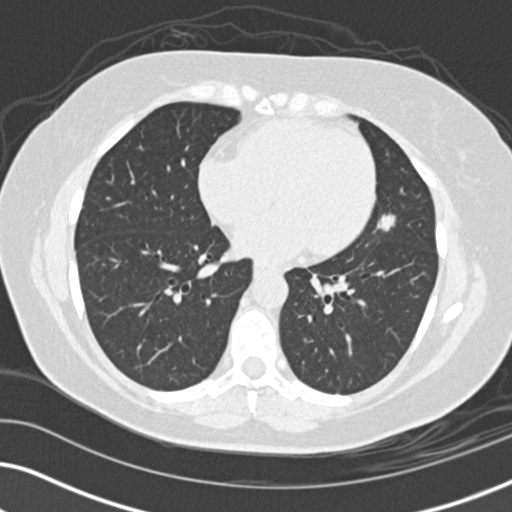
Low-dose screening chest CT, one axial slice; slice 69 of 152 in the series (ordered by position); reconstruction kernel B30f; 120 kVp; lung window (W 1500 / L -600 HU); 2 mm slice thickness; 512 × 512 image matrix.
Structures marked on this image (outlined manually by an expert reader):
- lesion 1 (tumor, upper lobe of left lung): bounding box <377,213,396,231> (left, top, right, bottom; pixels)